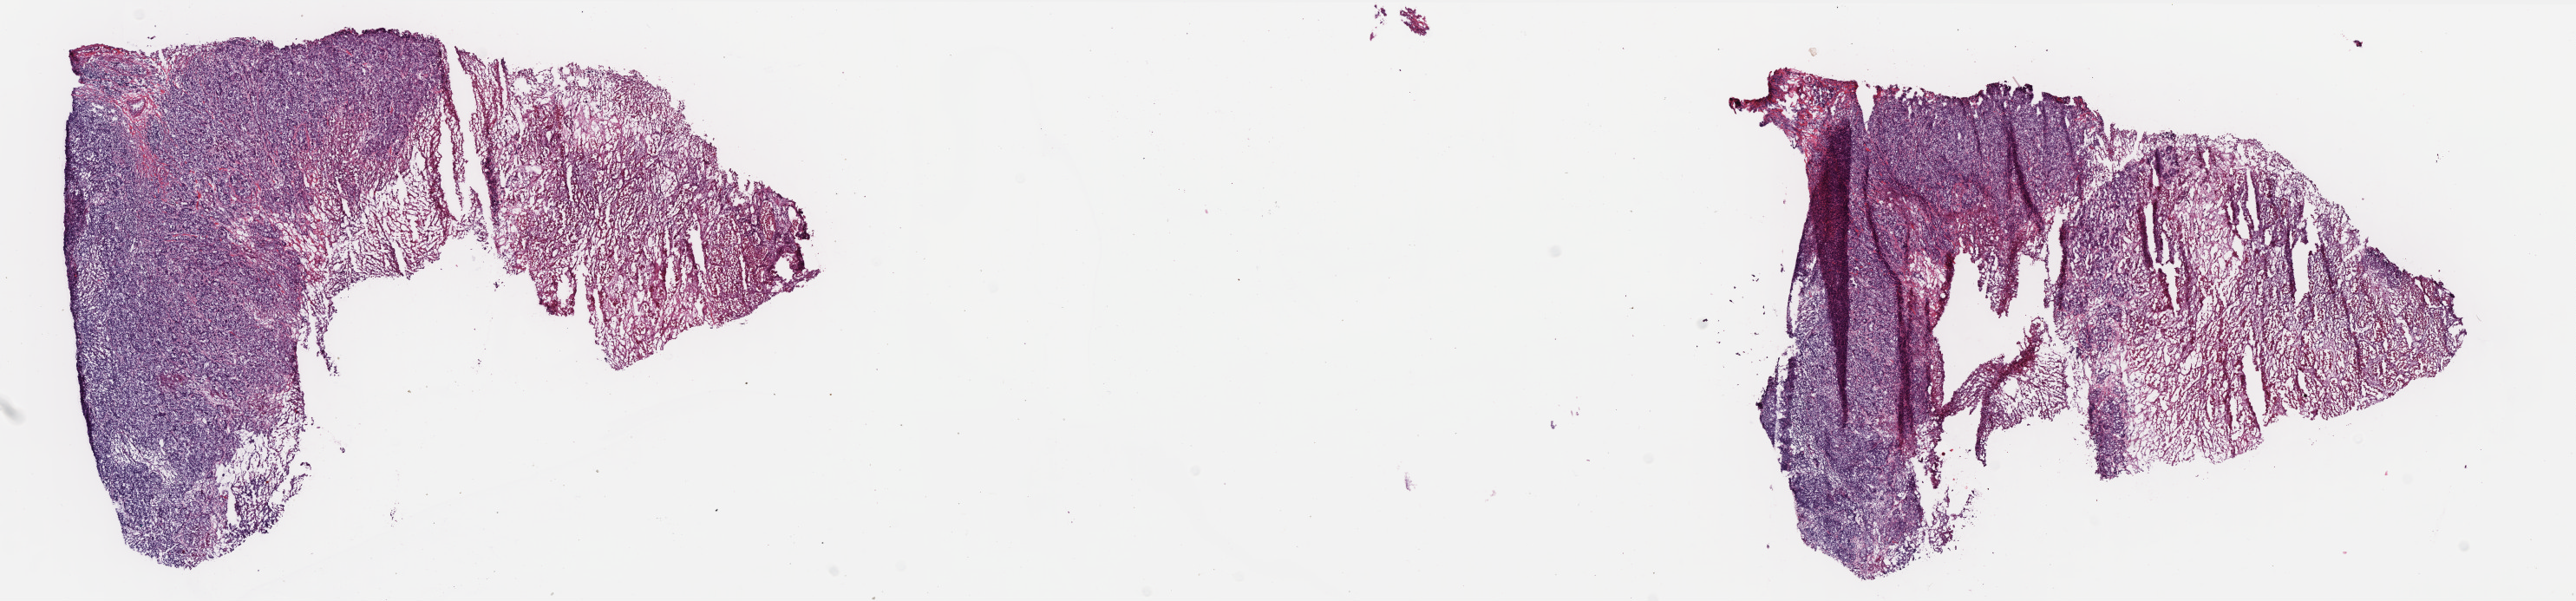
Digitized Hematoxylin and eosin (H&E) stained tissue section (whole slide), whole scanned area (about 23.8 x 5.6 mm, from a 40x scan) shown as a low-resolution overview. Frozen section from the bottom of the tissue portion. Breast, primary tumour sample. Patient: female, age at initial diagnosis 62 years. Composition of this section per pathologist review: tumour cells 57%, tumour nuclei 75%, normal cells 1%, stromal cells 12%, necrosis 30%. Inflammatory infiltration, as recorded: lymphocyte infiltration 18%, monocyte infiltration 0%, neutrophil infiltration 0%.
AJCC pathologic stage: IIA. Histologic diagnosis: Infiltrating duct carcinoma, NOS. Laterality: right. Lymph nodes positive (case pathology): 0 of 10 examined.